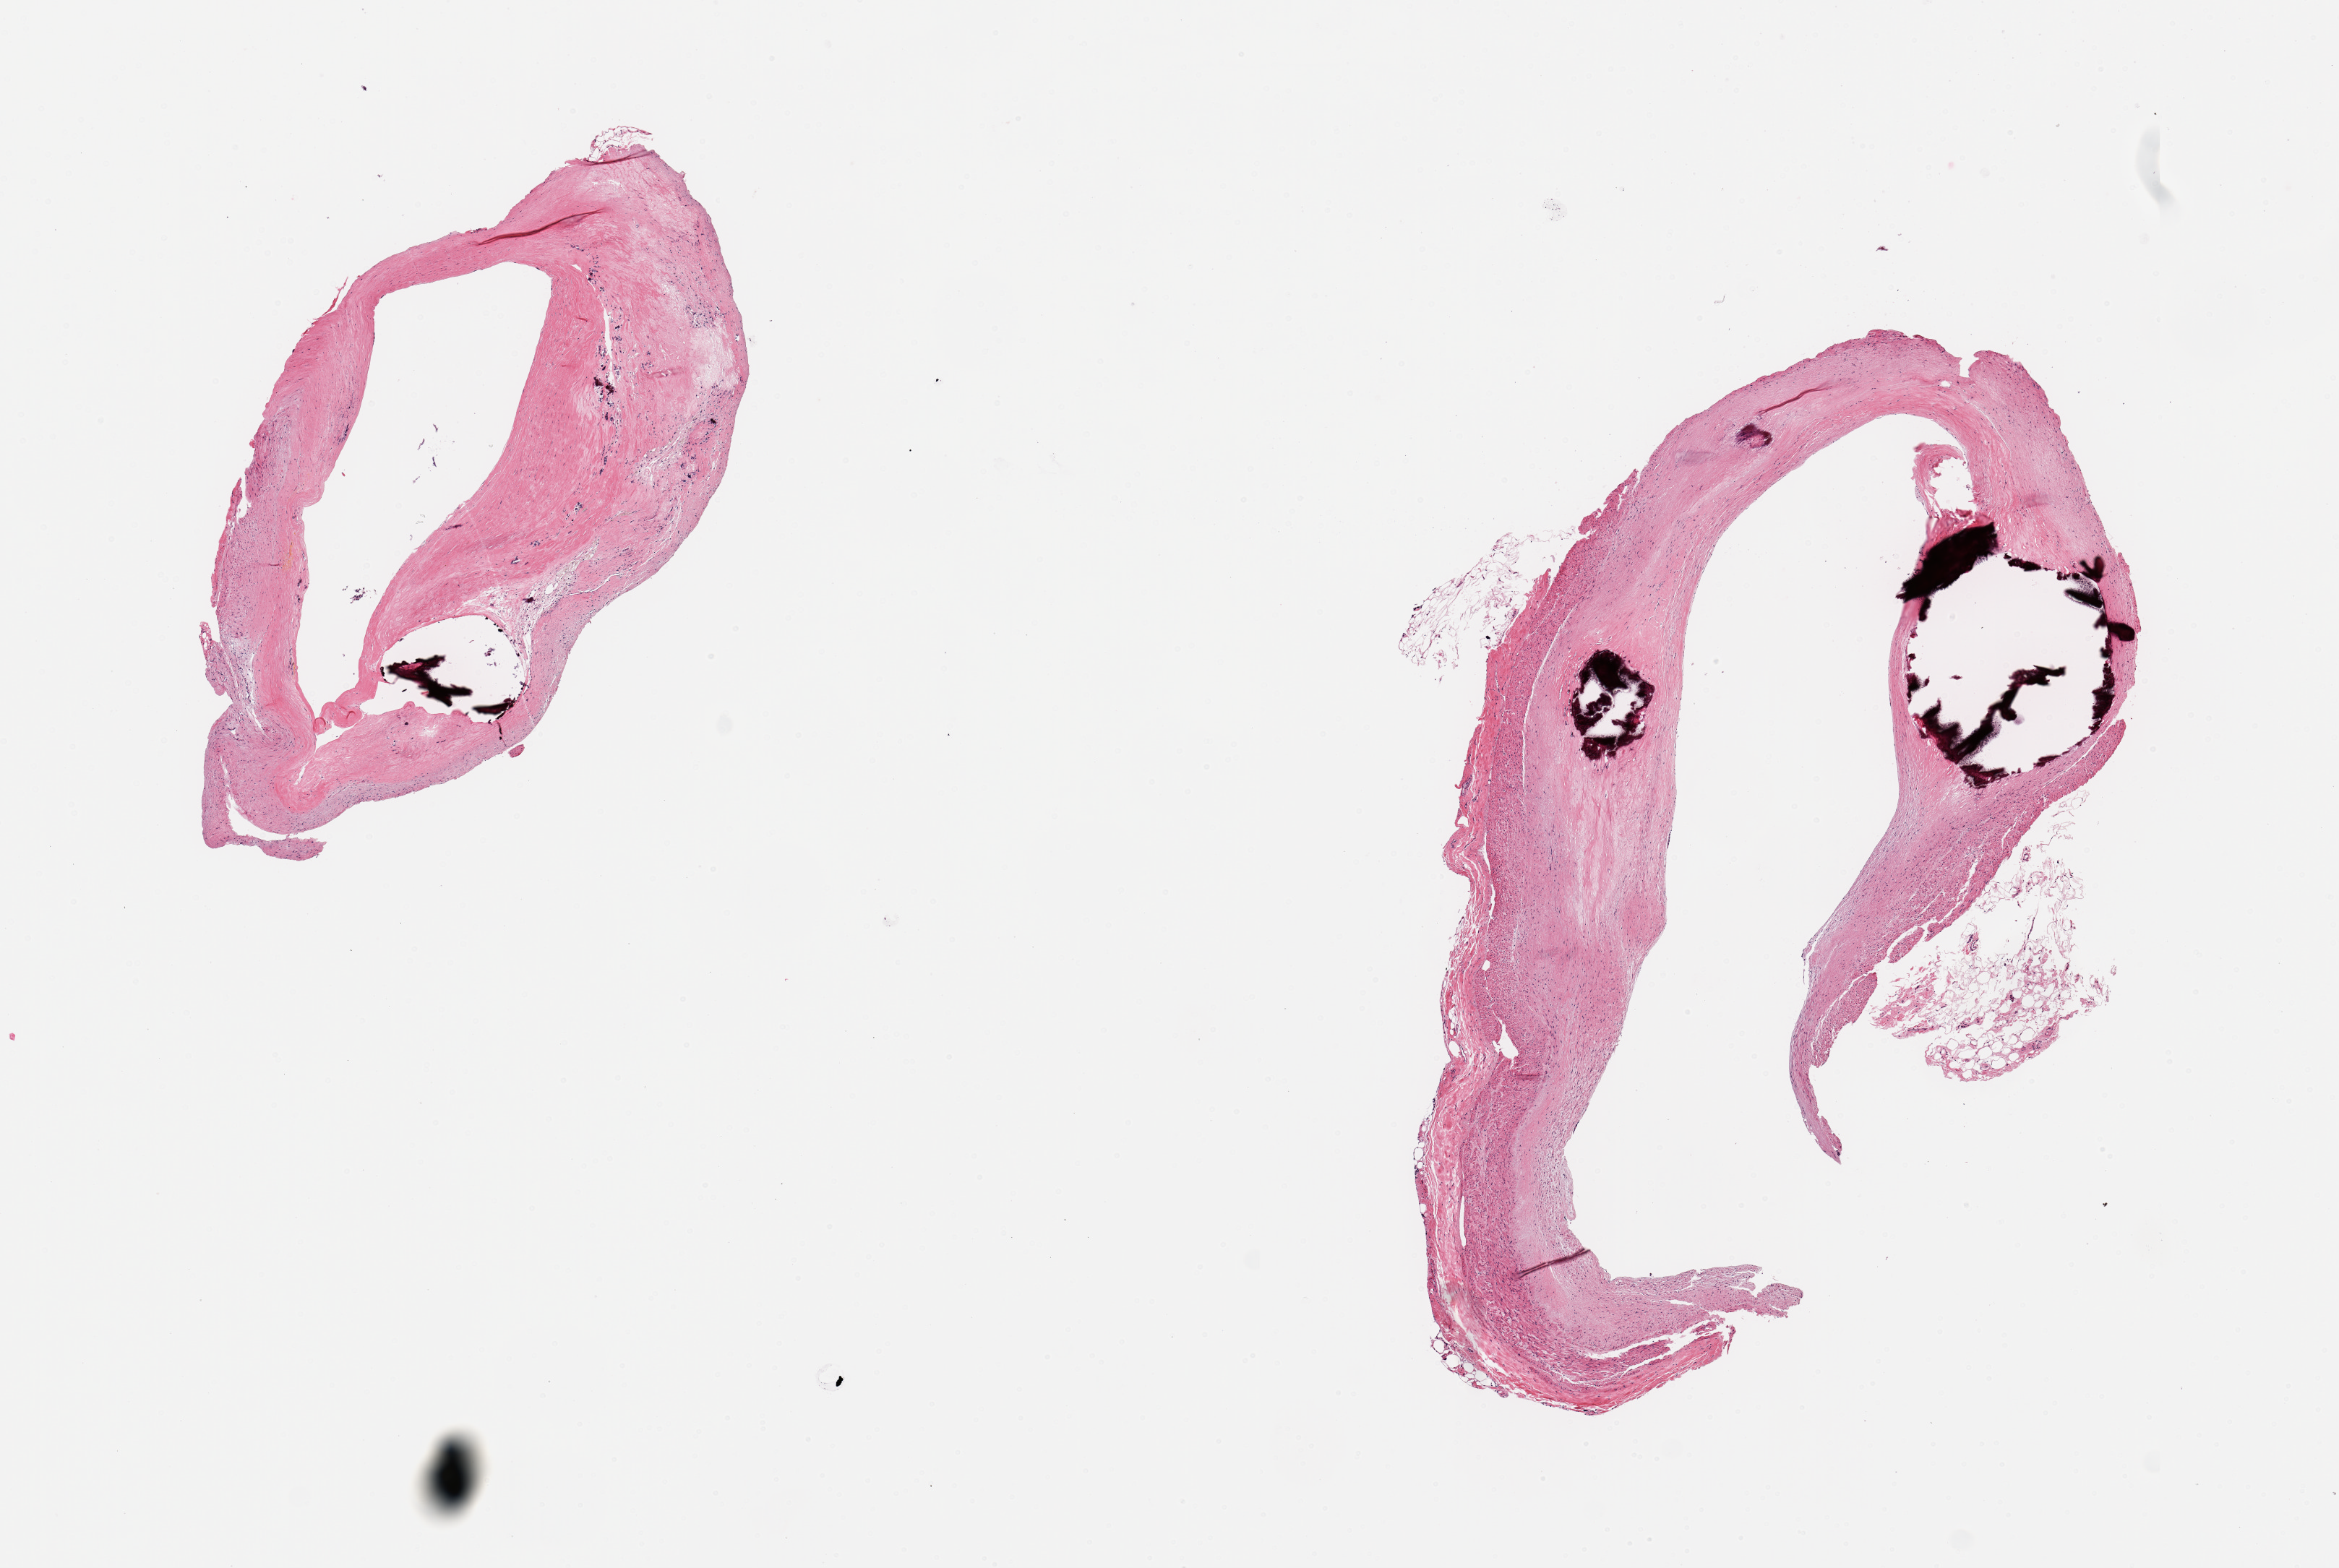
H&E whole-slide image, brightfield, low-resolution overview of the scanned area, about 12.8 x 8.6 mm. PAXgene-fixed paraffin-embedded (PFPE) section. Sampled site (target tissue): coronary artery. Donor tissue sample.
Pathologist's review note for this sample: 2 pieces; extensive atherosclerotic calcified plaques; <25% muscle.